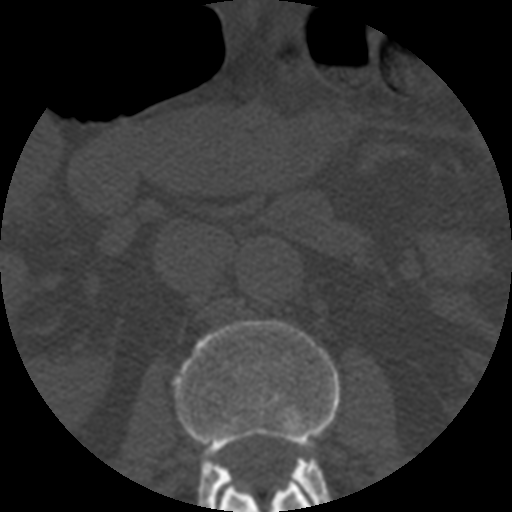
CT including the spine, one axial slice; position 164 of 508 along the scan axis; reconstruction kernel STANDARD; 120 kVp; bone window (W 1800 / L 400 HU); 1.25 mm slice thickness; 512 × 512 image matrix, field of view 160 × 160 mm. Patient age 57 years. From the clinical record (not read from this slice): primary cancer: prostate.
Structures marked on this image (semi-automatic segmentation, software-assisted and operator-edited):
- L1 vertebra: bounding box [x1, y1, x2, y2] px = [220, 481, 314, 512]
- L2 vertebra: [172, 320, 340, 512]